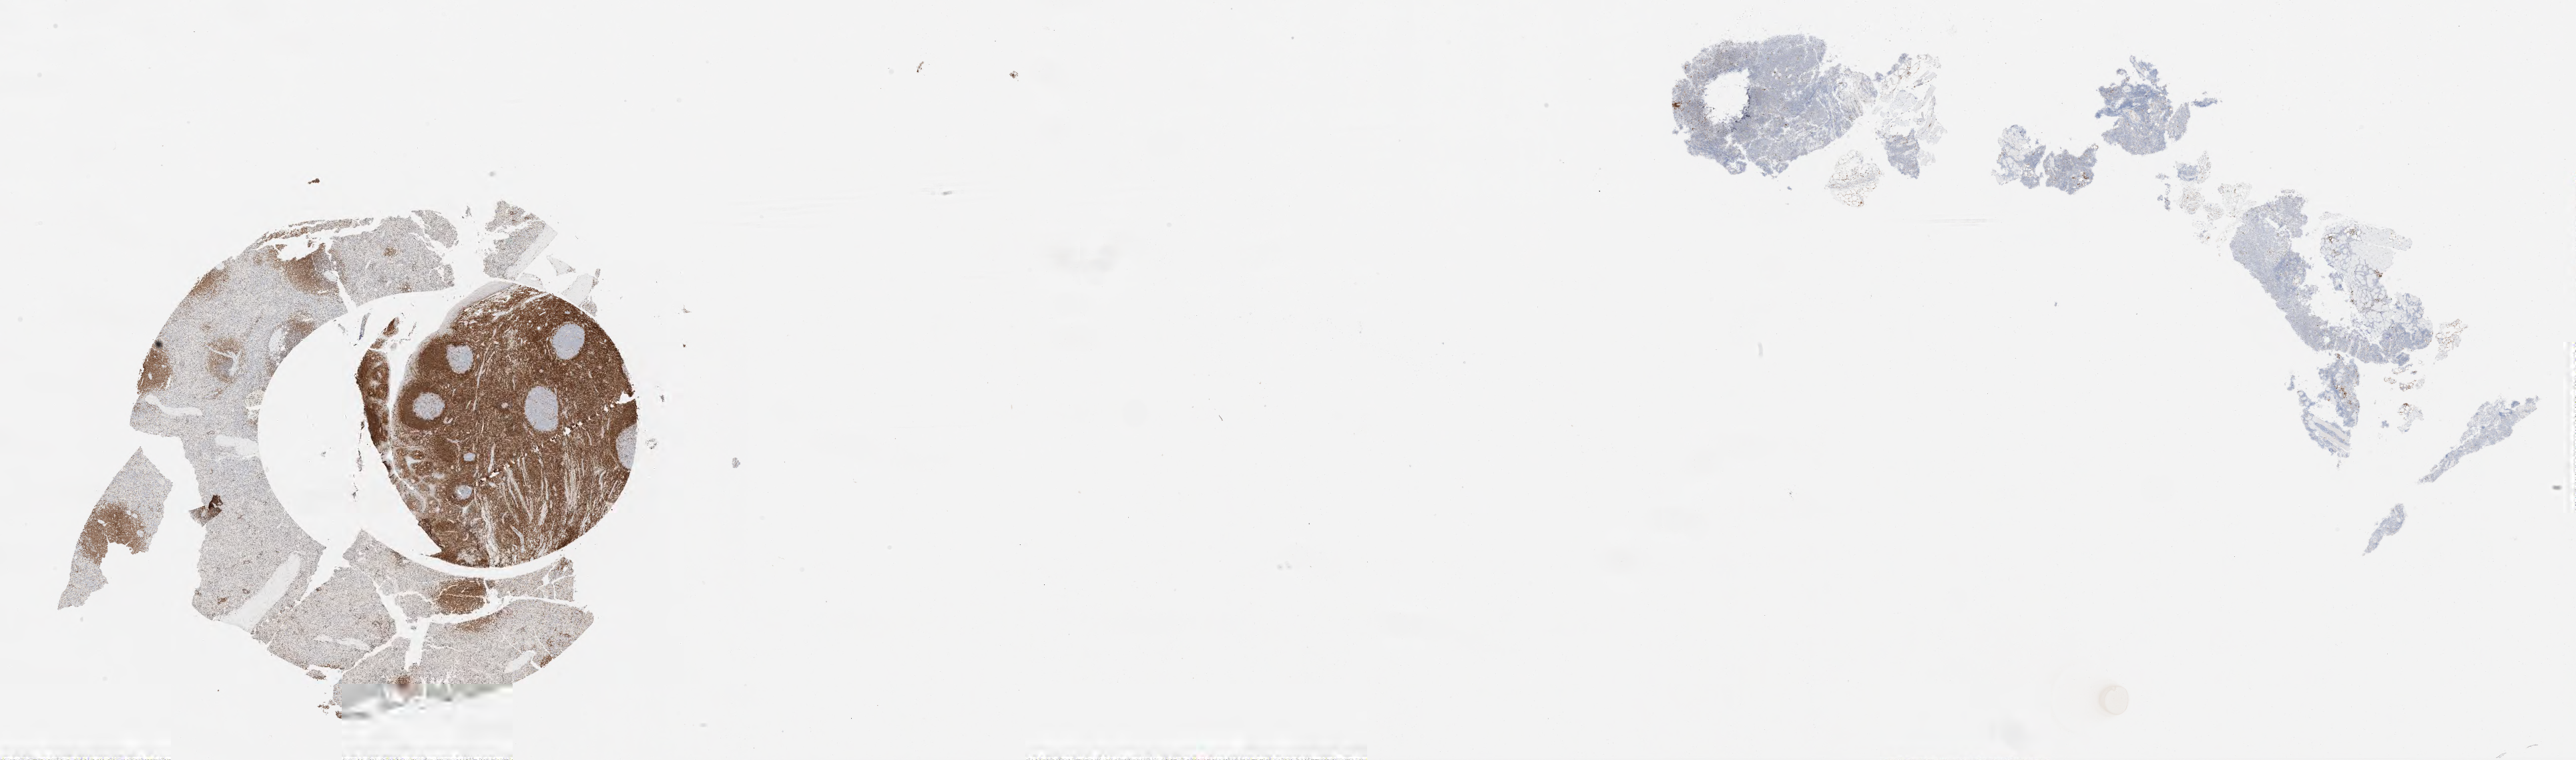
Immunohistochemistry (IHC) whole-slide image stained for BCL2 — a low-resolution overview of the entire scanned area, about 31.0 x 9.1 mm. Tumor tissue. Patient: female, age 69 years.
Diagnosis: Burkitt lymphoma, NOS.